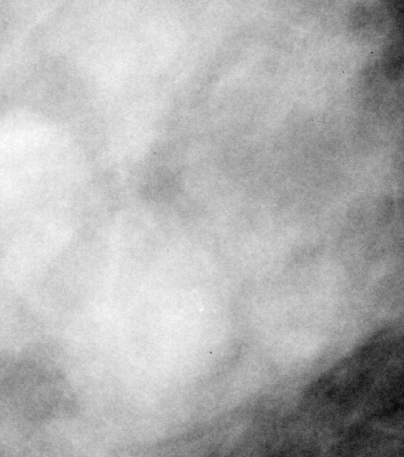
Region of interest cut from a scanned film mammogram (one marked finding), right breast, MLO view, BI-RADS breast density category 3 (scale 1–4).
Mass, shape lobulated, margins obscured; BI-RADS assessment category 3; pathology result (as recorded, not read from the image): benign.